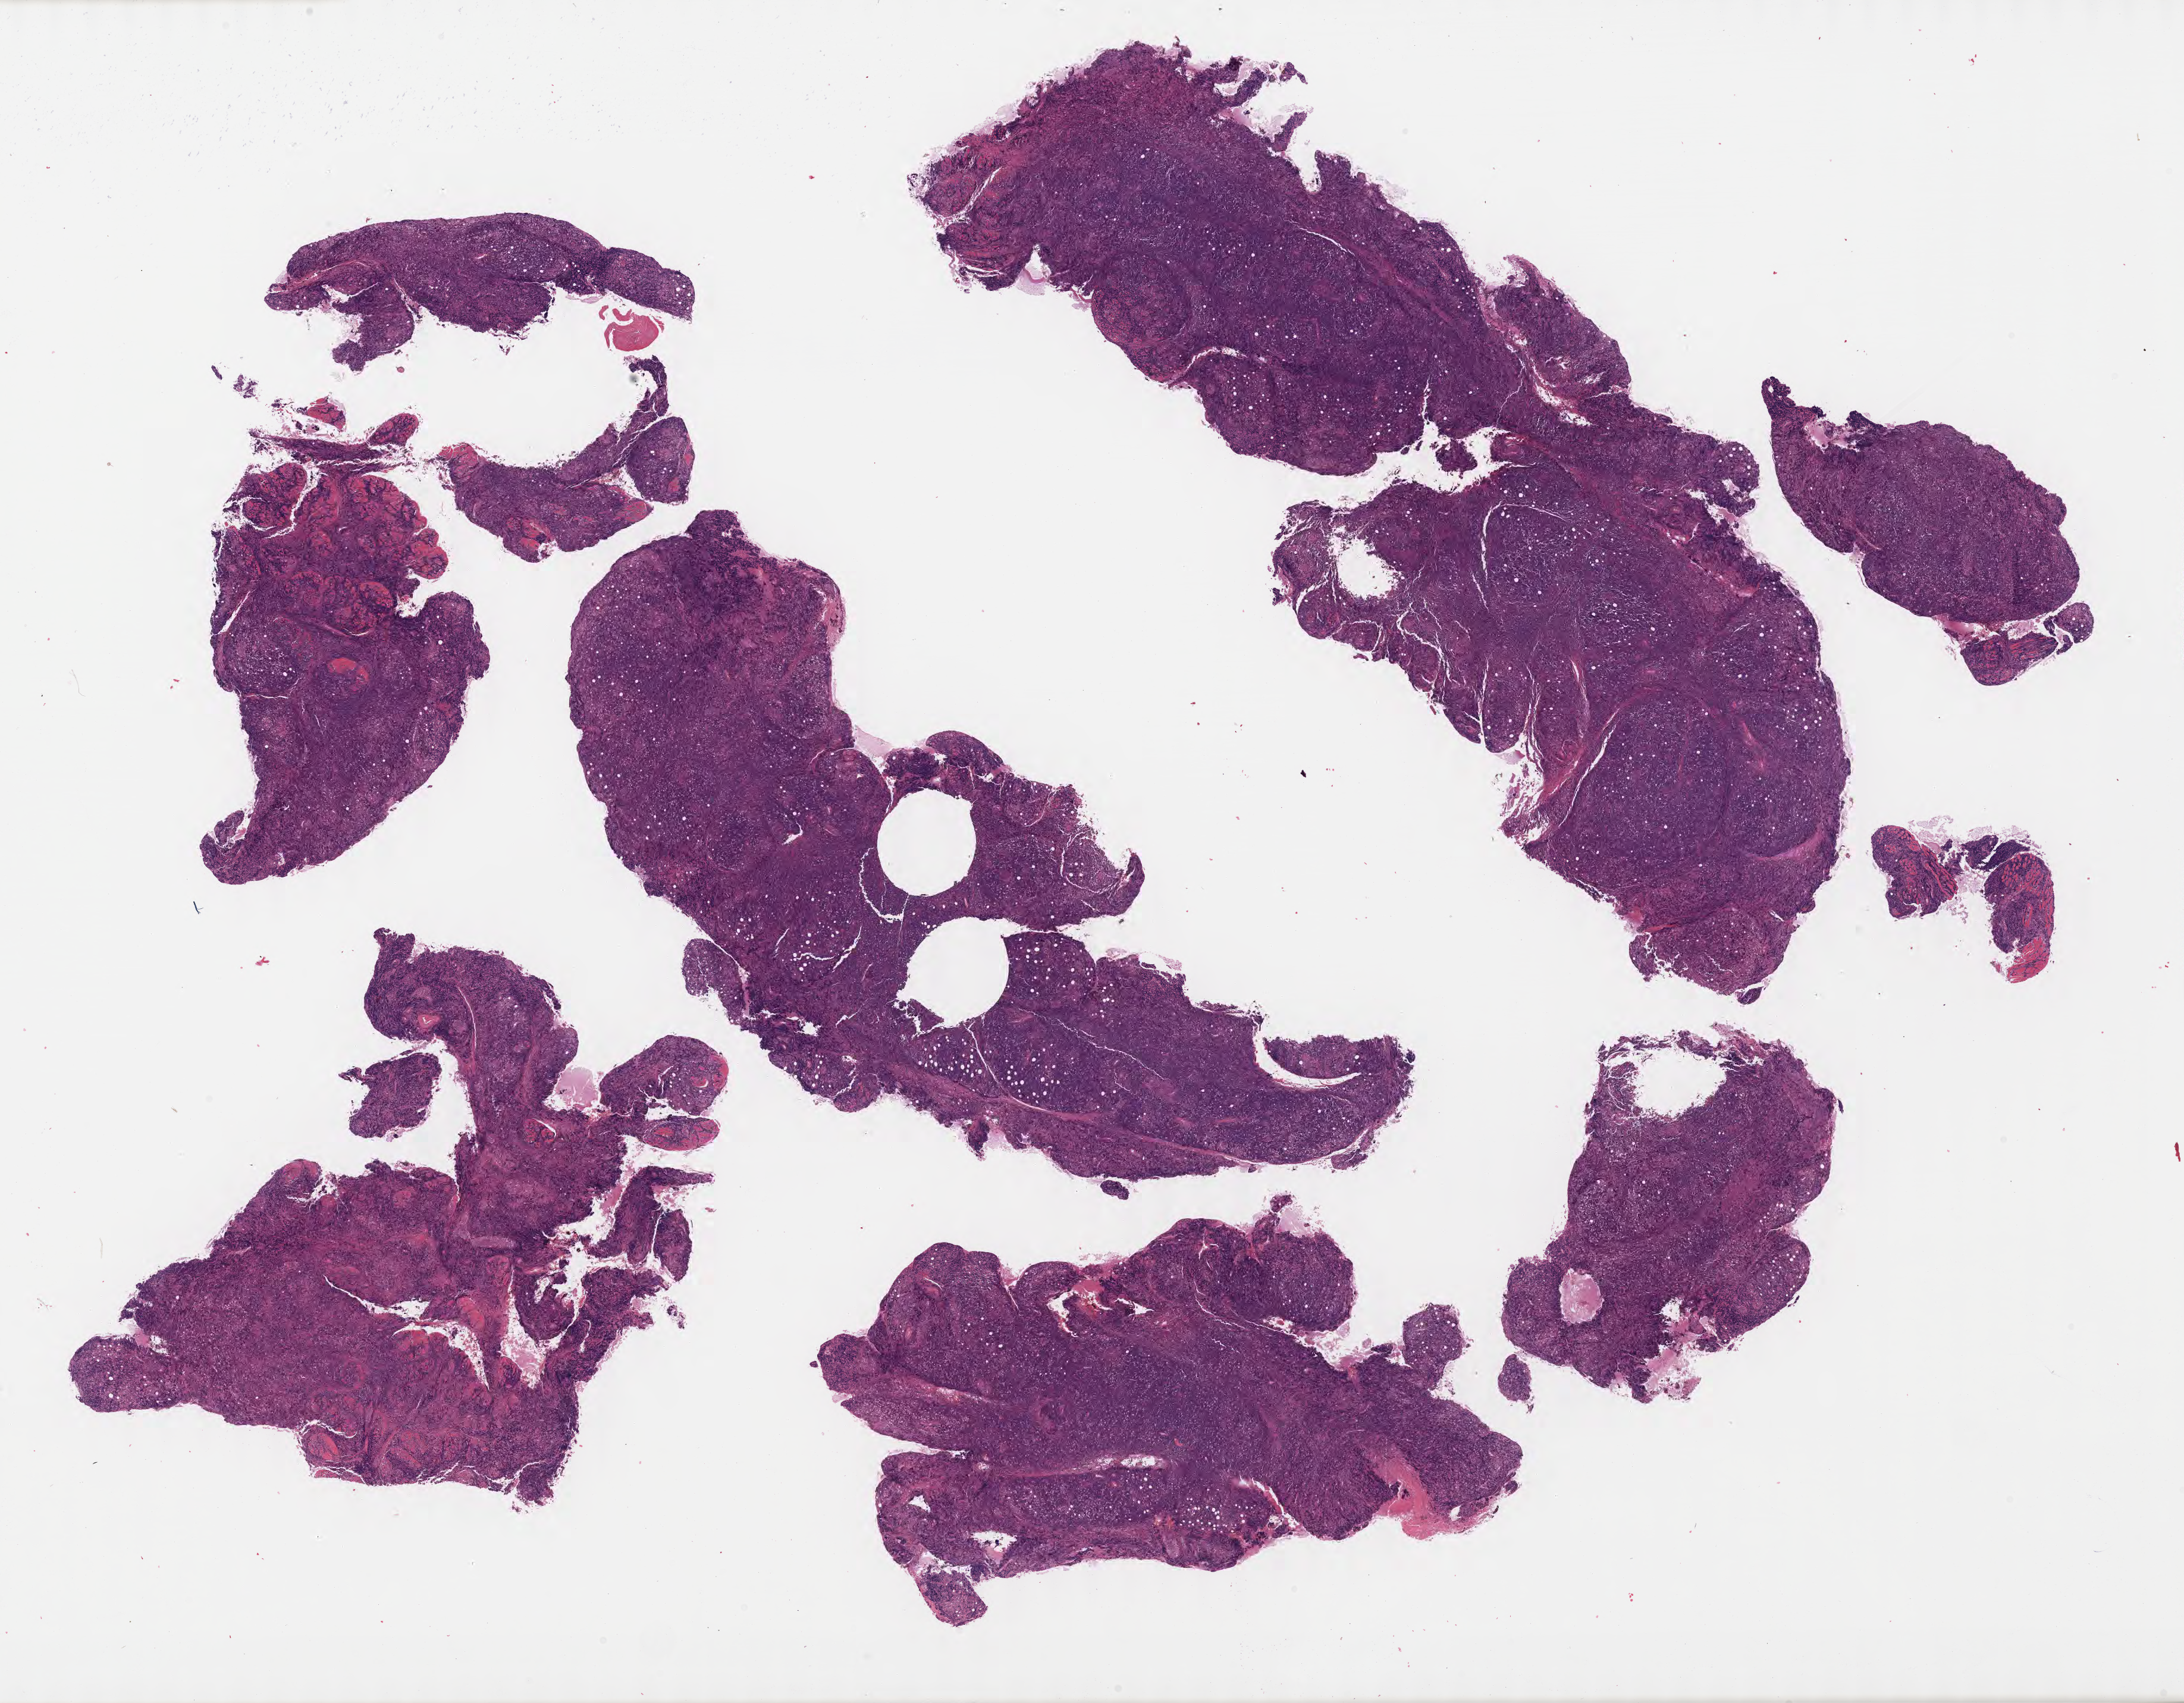
Digitized hematoxylin and eosin (H&E)-stained section, low-resolution overview of the scanned area, about 29.7 x 23.1 mm. Specimen: tumor tissue. Anatomic site: cranium. Patient: male, age at initial diagnosis 5 years.
Histologic diagnosis: Burkitt lymphoma, NOS.